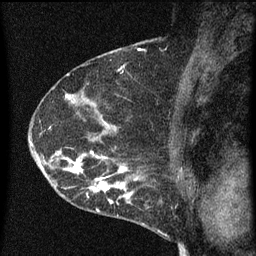
Breast MRI (dynamic contrast-enhanced), one sagittal slice; position 43 of 60 along the scan axis; dynamic contrast-enhanced series, image 2 of 3 at this slice position (ordered by acquisition); 1.5 T; TE 4.2 ms, TR 8 ms; 2 mm slice thickness; 256 × 256 image matrix. Patient: female, 54 years.
Structures marked on this image (semi-automatic segmentation, software-assisted and operator-edited):
- analysis volume of interest (the breast-tissue region the enhancement analysis was run in; not a lesion): box from (x=49, y=138) to (x=164, y=209) px
- tumour enhancement mask (voxels above the 70 % enhancement threshold inside the analysis volume of interest): (x=49, y=150)–(x=150, y=209)